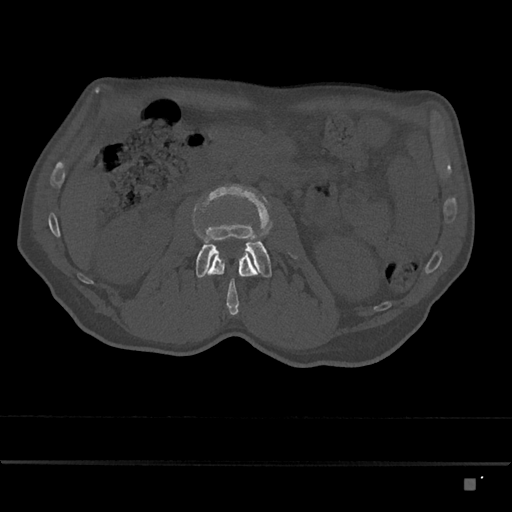
CT including the spine, one axial slice. Bone window (W 1800 / L 400 HU). 512 × 512 image matrix, field of view 390 × 390 mm. Male patient, age 72 years. From the clinical record (not read from this slice): primary cancer: prostate.
Annotated regions visible in this slice (semi-automatically segmented with operator editing):
- L2 vertebra: bounding box [x1, y1, x2, y2] px = [203, 248, 258, 315]
- L3 vertebra: [193, 184, 297, 278]